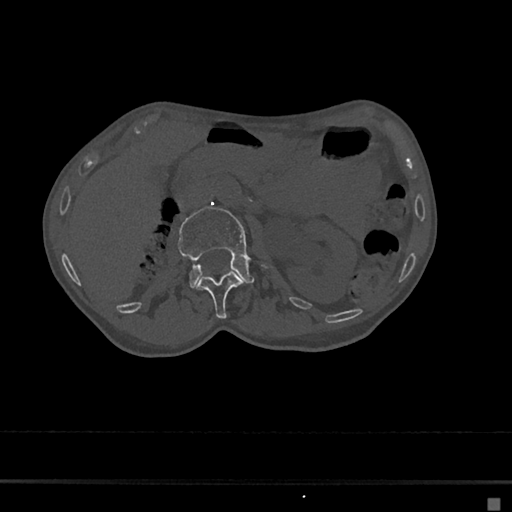
CT including the spine, one axial slice. Slice 41 of 797 in the series (ordered by position). 120 kVp. Bone window (W 1800 / L 400 HU). 512 × 512 image matrix, field of view 360 × 360 mm. Female patient, age 68 years. From the clinical record (not read from this slice): primary cancer: renal.
Outlined on this slice (semi-automatic segmentation, software-assisted and operator-edited):
- L1 vertebra: bounding box [x1, y1, x2, y2] px = [196, 271, 242, 319]
- L2 vertebra: [178, 206, 253, 287]